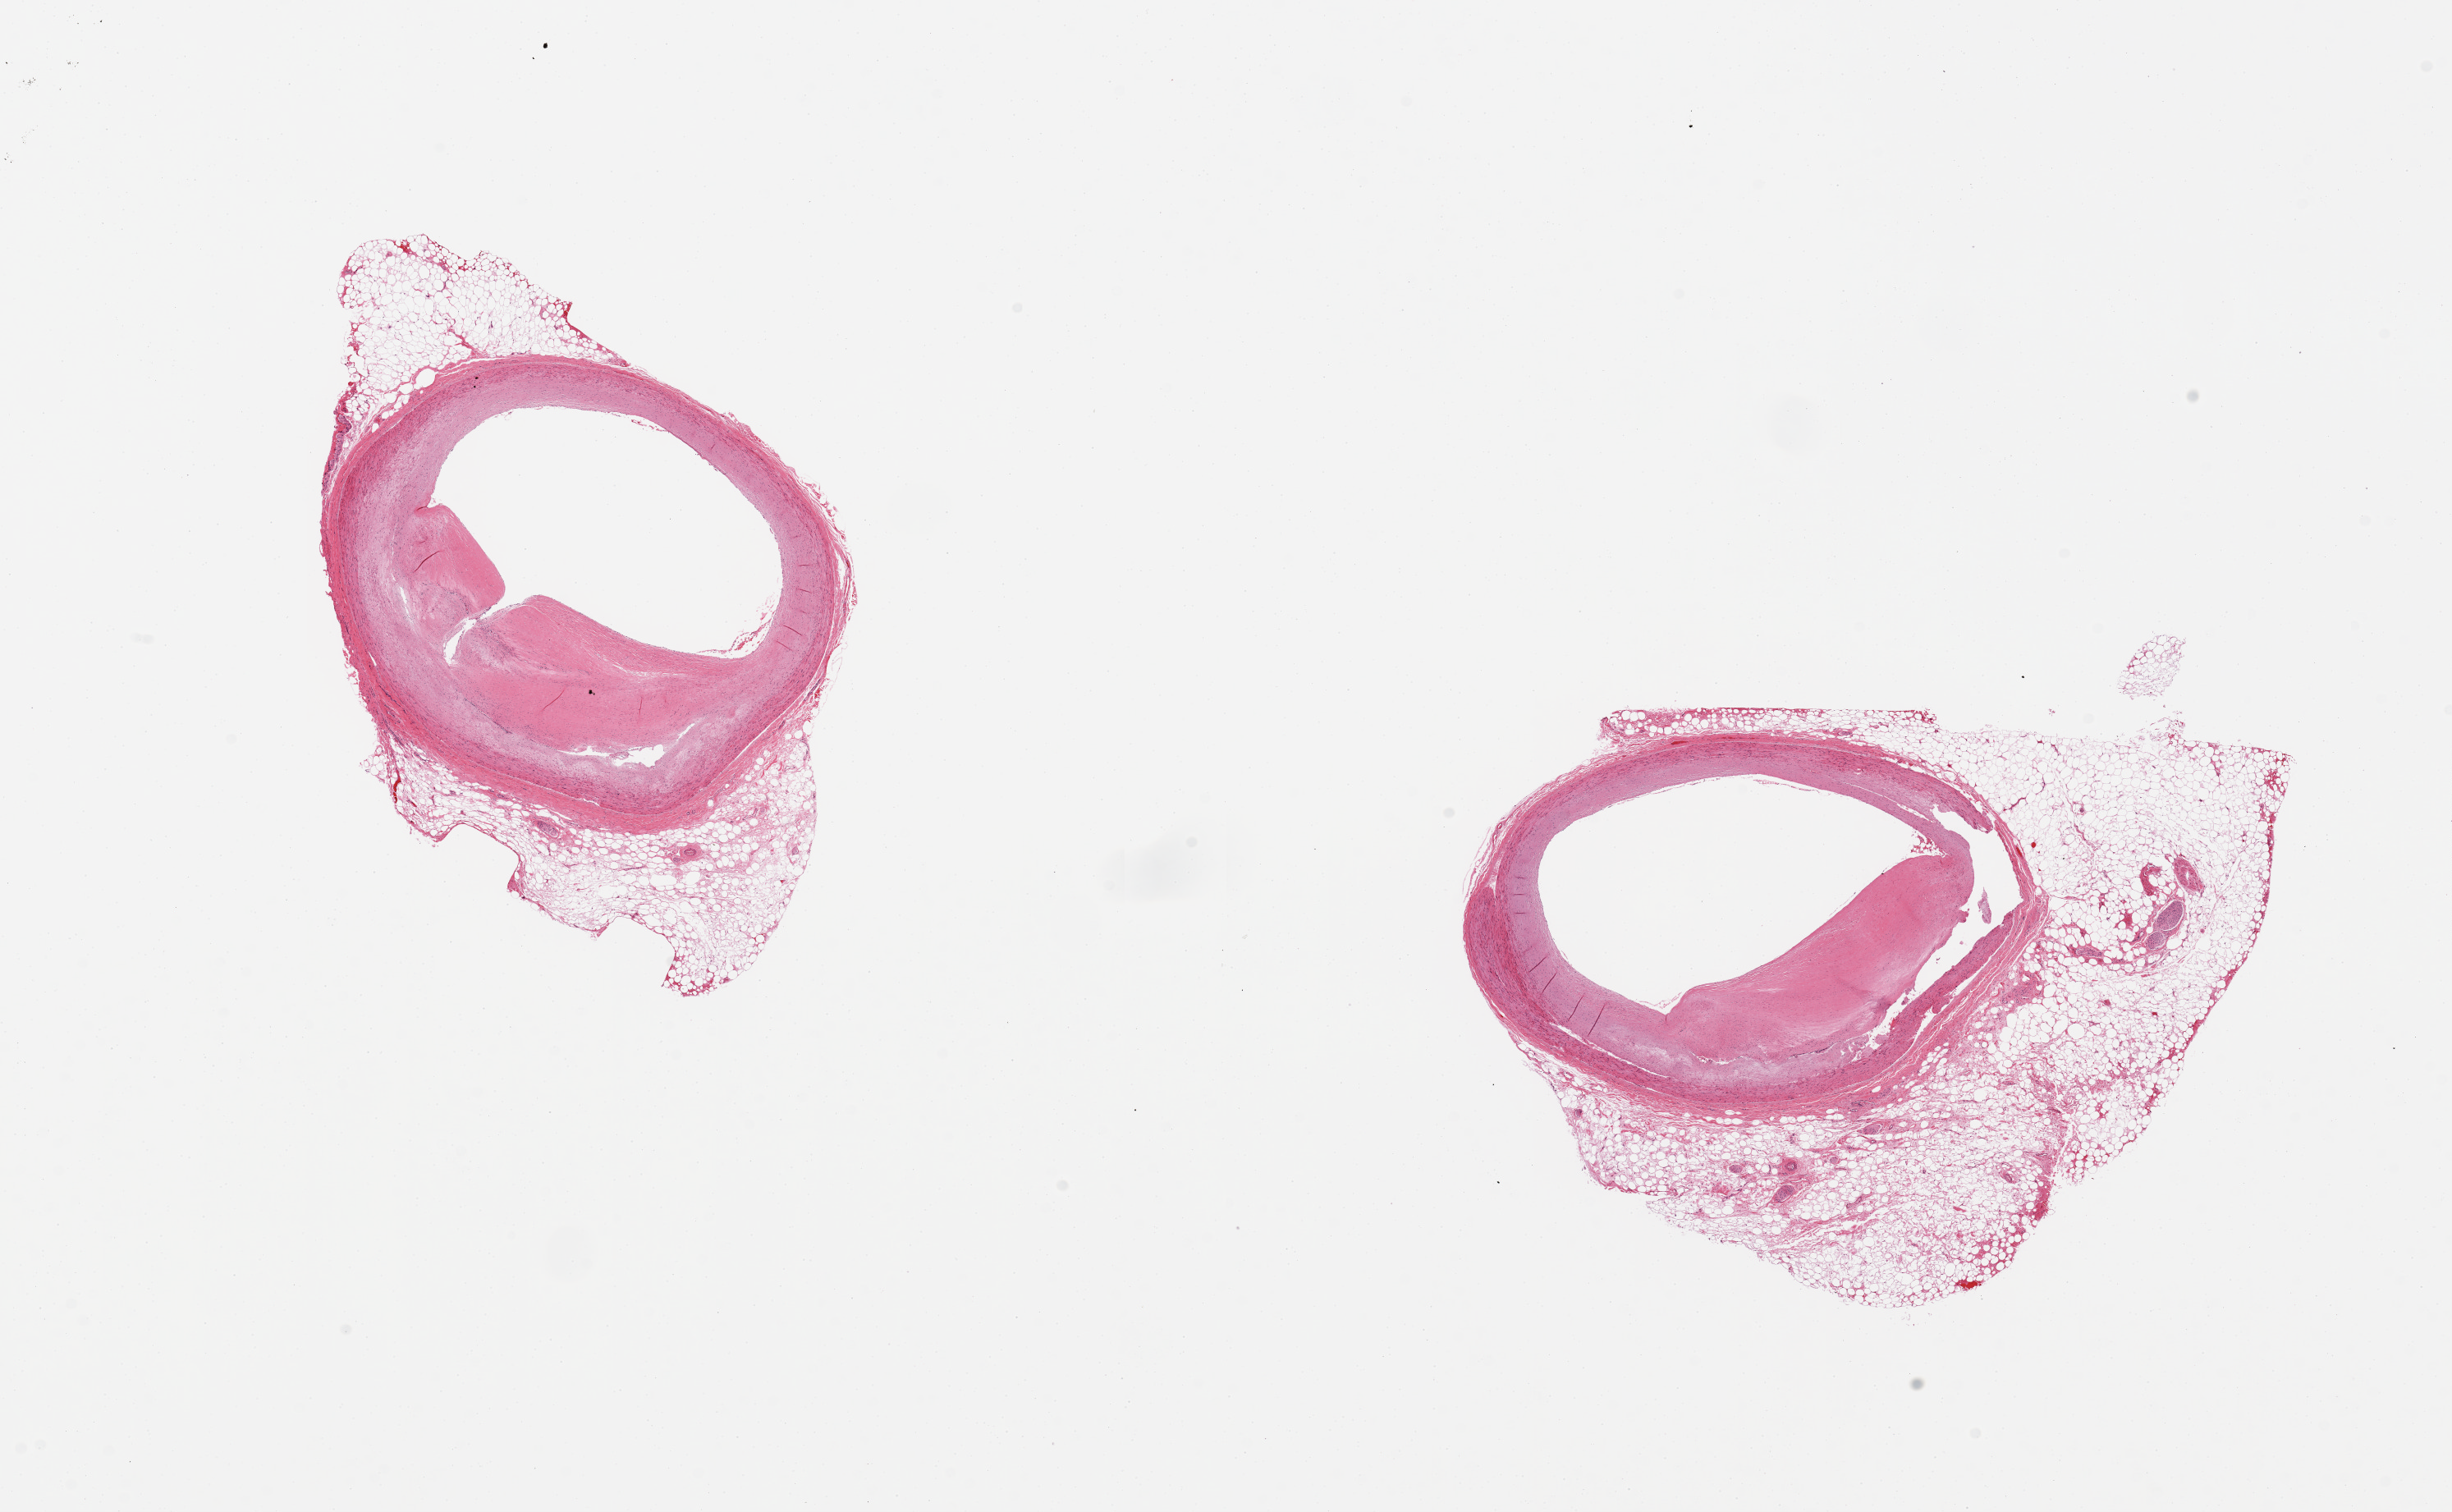
Whole-slide image, hematoxylin and eosin (H&E) stain, brightfield, low-resolution overview of the scanned area, about 23.6 x 14.6 mm (from a 20x scan). PAXgene-fixed, paraffin-embedded tissue. Target tissue: coronary artery. Donor tissue sample. Male donor.
* reviewer comment on this tissue sample: 2 pieces; patent but atherosclerotic; 40-50% peripheral fat